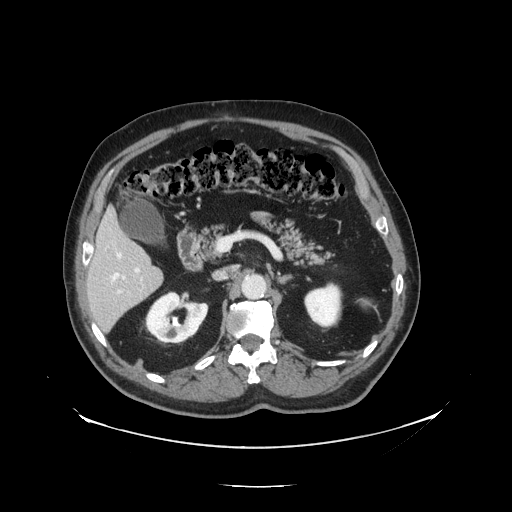
Contrast-enhanced abdominal CT, one axial slice. Slice 70 of 138 in the series (ordered by position). Reconstruction kernel STANDARD. 120 kVp. Intravenous contrast given. Soft-tissue window (W 400 / L 40 HU). 2.5 mm slice thickness. 512 × 512 image matrix, field of view 497 × 497 mm. Male patient, age 77 years. From the clinical record (not read from this slice): diagnosis: colorectal cancer liver metastases, imaged before liver resection; multiple liver metastases: no; largest metastasis: 1.5 cm; disease in both lobes: no.
Outlined on this slice (manually delineated by an expert):
- hepatic veins: bounding box [x1, y1, x2, y2] px = [111, 253, 125, 281]
- liver: [88, 213, 162, 332]
- planned liver remnant (the part of the liver to remain after resection): [88, 213, 153, 286]
- portal vein (with intrahepatic branches): [116, 267, 140, 294]